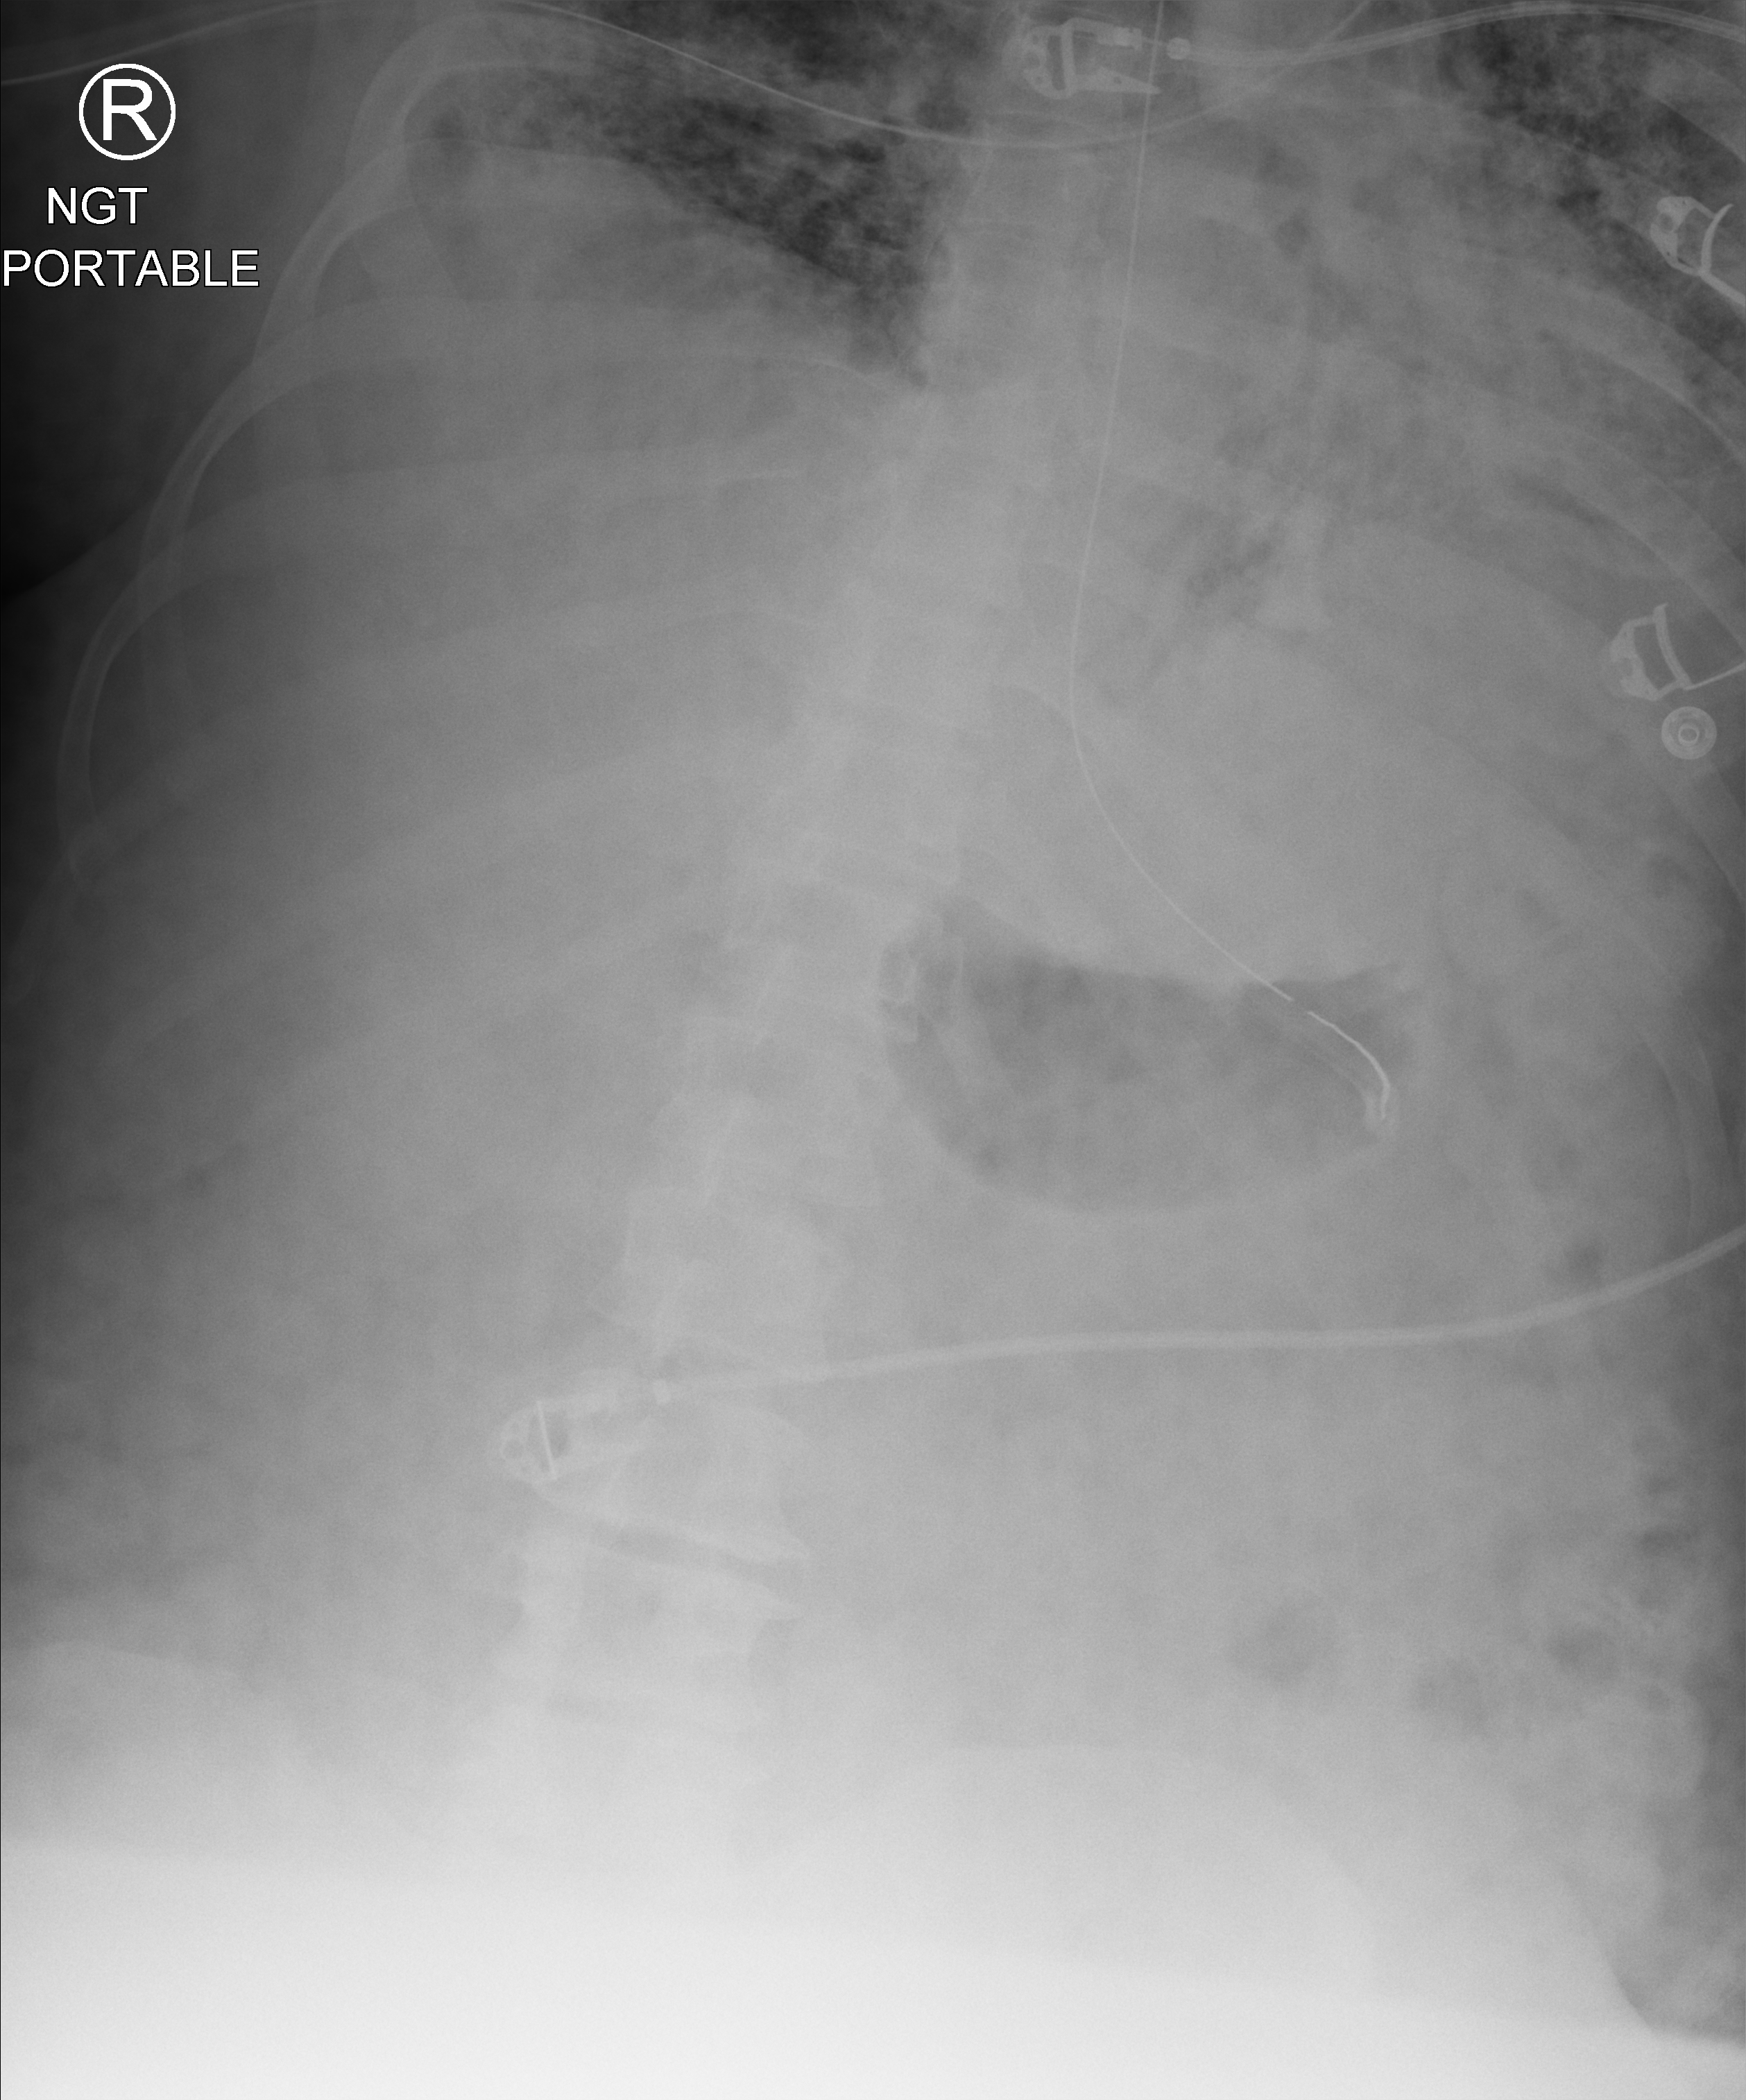
Bedside abdomen radiograph (computed radiography), anteroposterior (AP) projection. Male patient hospitalised with COVID-19, age 18–59 years.
From the hospital-stay record, not from the radiograph (when in the stay this image was taken is not recorded): mechanically ventilated during this hospital stay: yes; admitted to intensive care during this hospital stay: yes; smoking status (admission record): never.